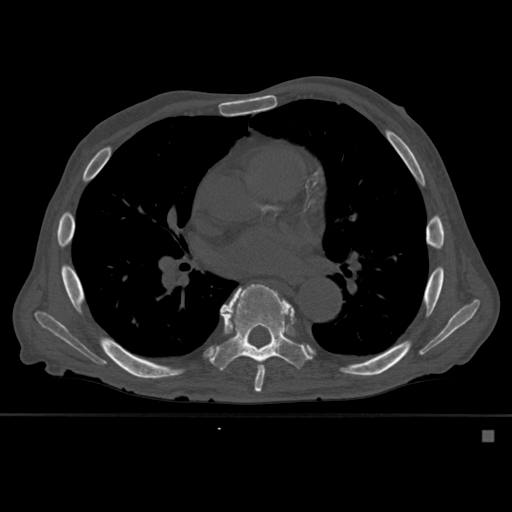
CT including the spine, one axial slice. Bone window (W 1800 / L 400 HU). 1.5 mm slice thickness. 512 × 512 image matrix, field of view 373 × 373 mm. Patient: male, 78 years. From the clinical record (not read from this slice): primary cancer: prostate.
Structures marked on this image (semi-automatically segmented with operator editing):
- T7 vertebra: box from (x=224, y=287) to (x=265, y=392) px
- T8 vertebra: (x=209, y=284)–(x=309, y=371)